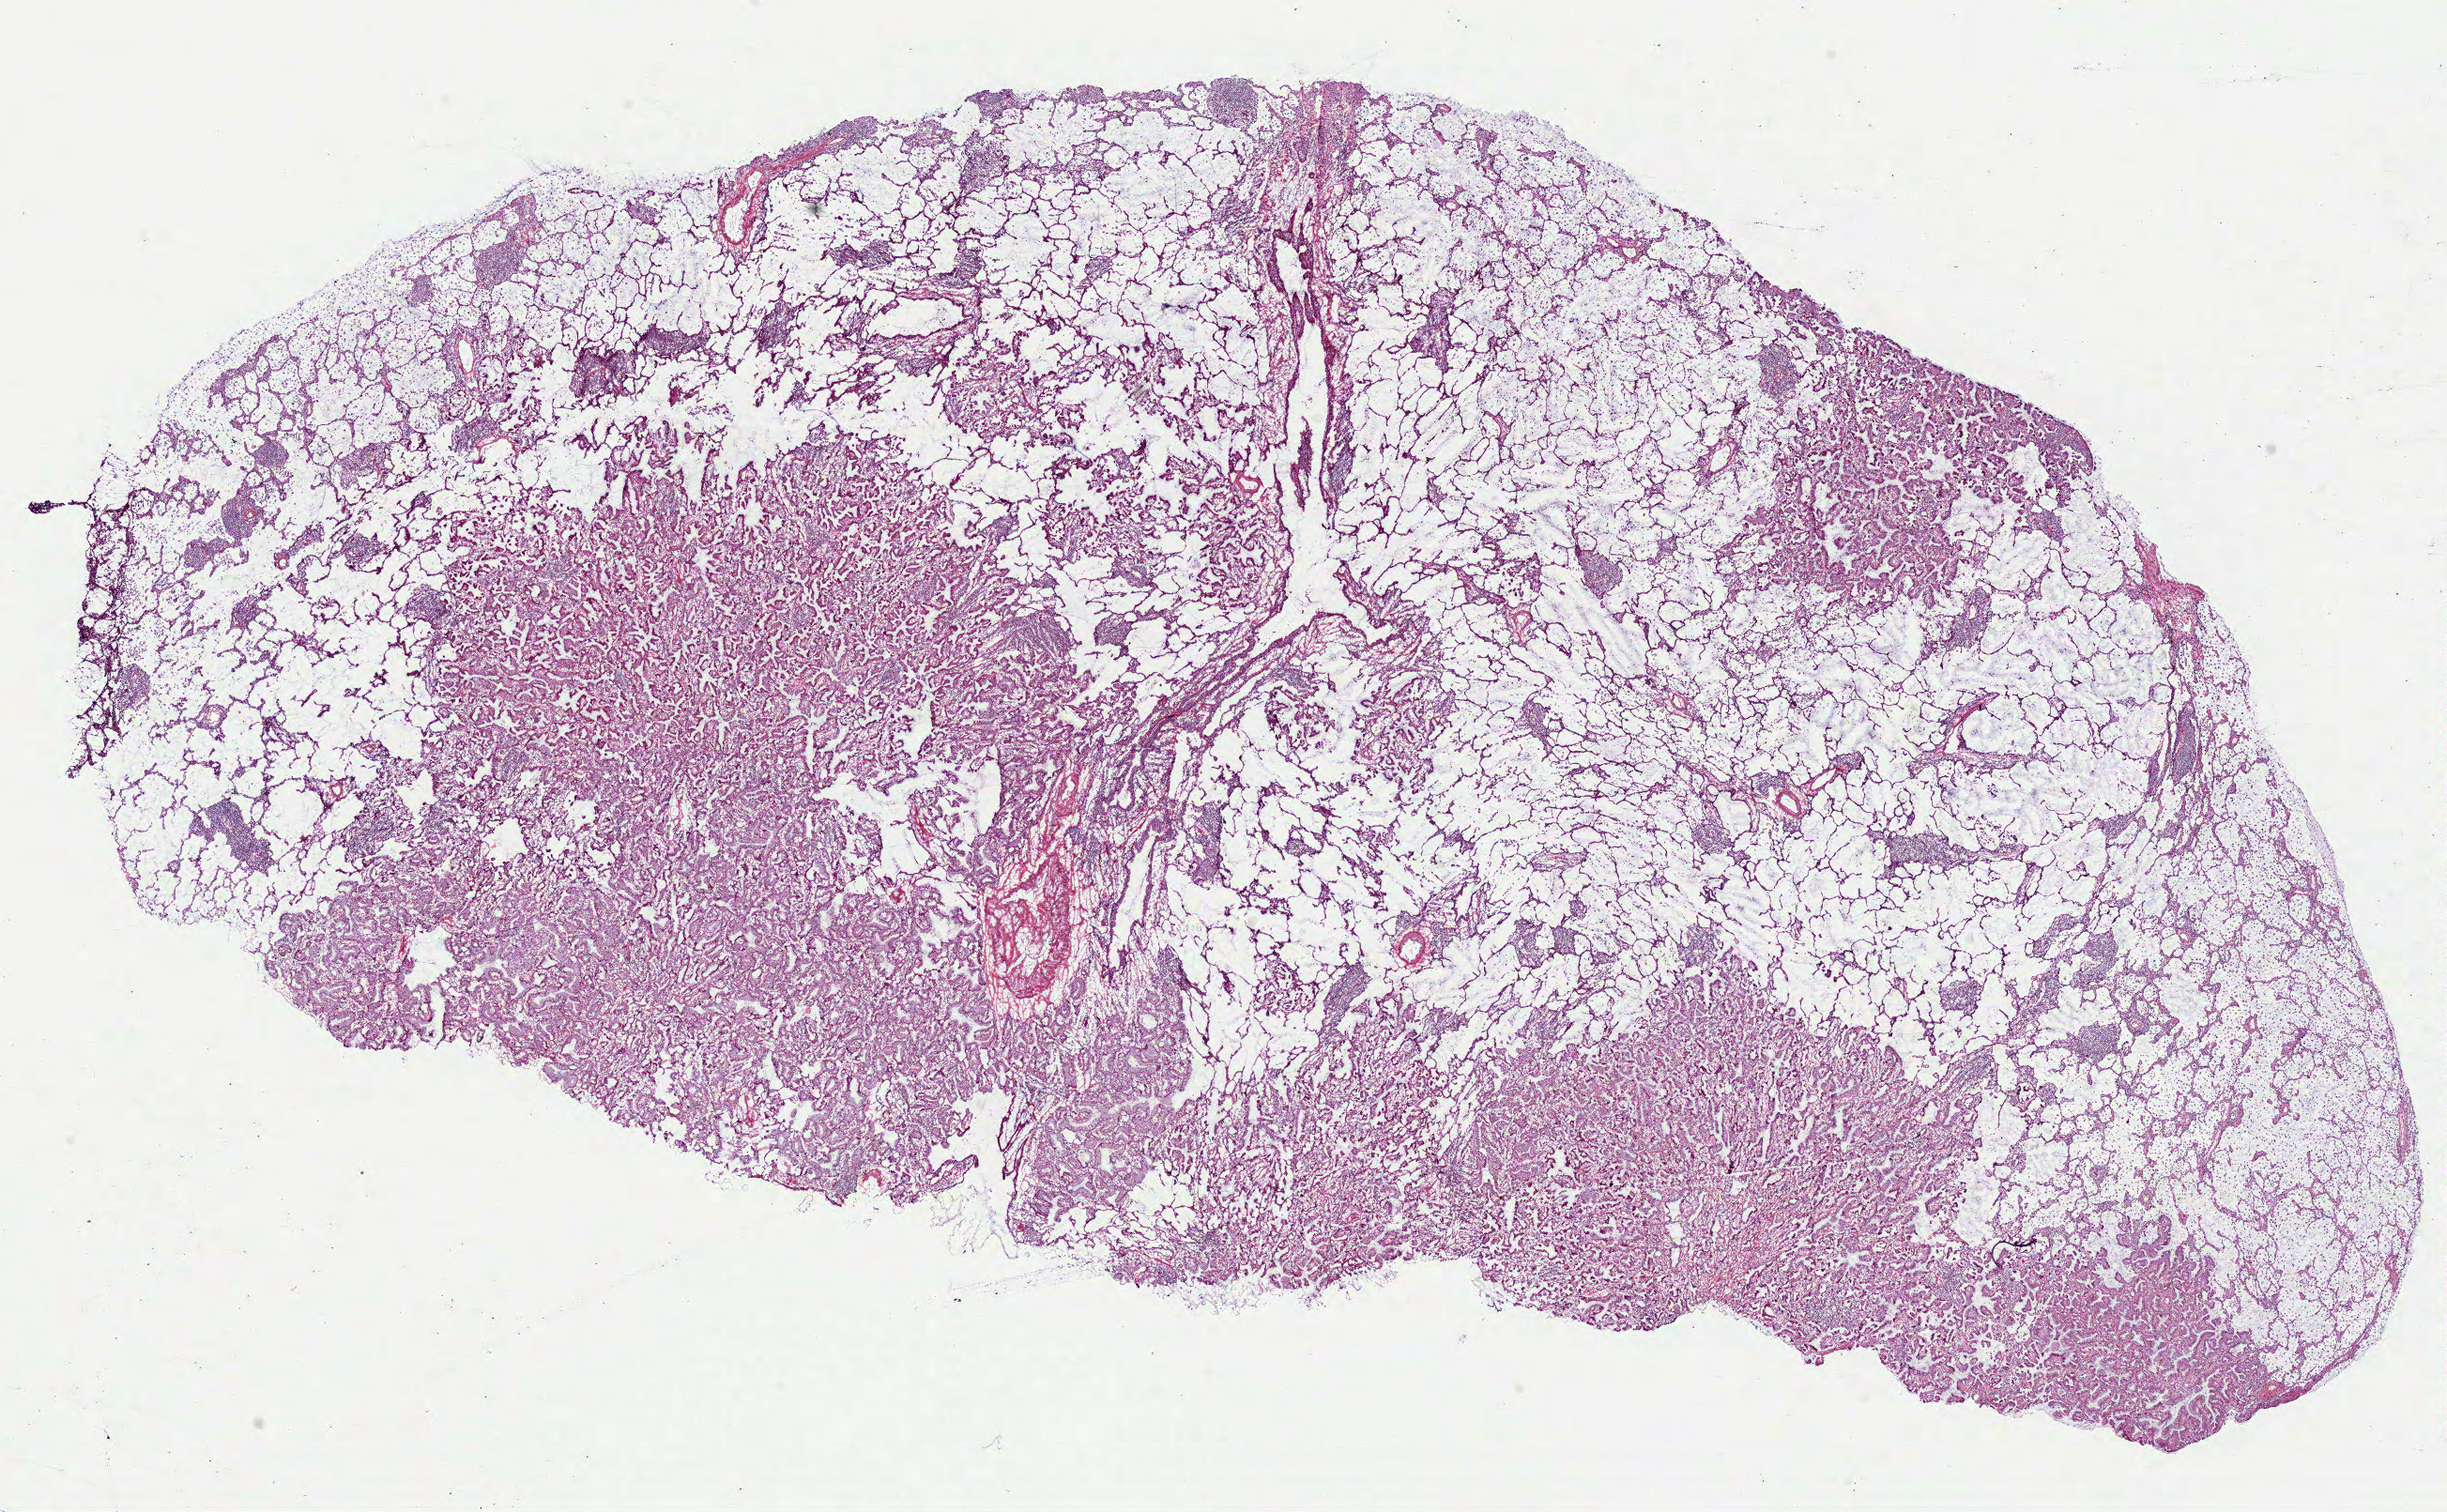
Whole-slide histology image, H&E, low-resolution overview of the scanned area, about 21.0 x 13.0 mm (acquisition: 40x scan), frozen section from the bottom of the tissue portion, primary tumour sample from the lung. Male patient; age at initial diagnosis 70 years. Pathologist review of this section (percent, as recorded): tumour cells 65%, tumour nuclei 50%.
Diagnosis: Bronchio-alveolar carcinoma, mucinous (lower lobe, lung).